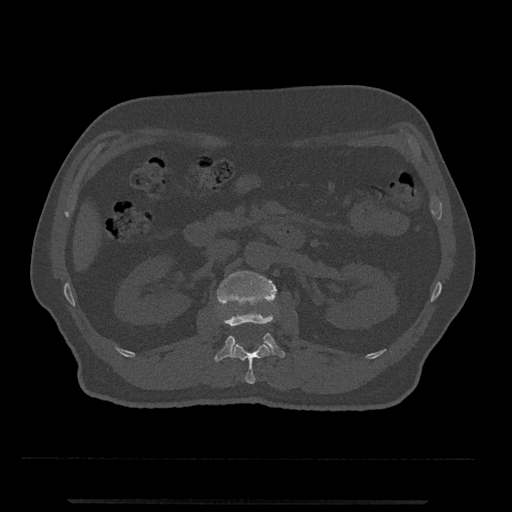
CT including the spine, one axial slice; position 298 of 797 along the scan axis; reconstruction kernel Br40s/3; 120 kVp; bone window (W 1800 / L 400 HU); 512 × 512 image matrix. Patient: male, 63 years. Case-level facts recorded for this patient, not image findings: primary cancer: prostate.
Annotated regions visible in this slice (semi-automatically segmented with operator editing):
- L1 vertebra: bounding box [x1, y1, x2, y2] px = [231, 343, 272, 384]
- L2 vertebra: [214, 270, 285, 362]